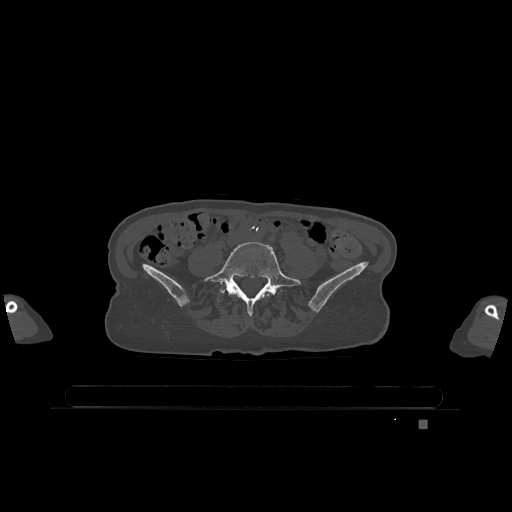
CT including the spine, one axial slice; position 246 of 1317 along the scan axis; bone window (W 1800 / L 400 HU); 512 × 512 image matrix, field of view 500 × 500 mm. Patient: female, 74 years. From the clinical record (not read from this slice): primary cancer: lung.
Structures marked on this image (semi-automatic segmentation, software-assisted and operator-edited):
- L4 vertebra: bounding box <265,294,270,297> (left, top, right, bottom; pixels)
- L5 vertebra: <204,242,301,315>